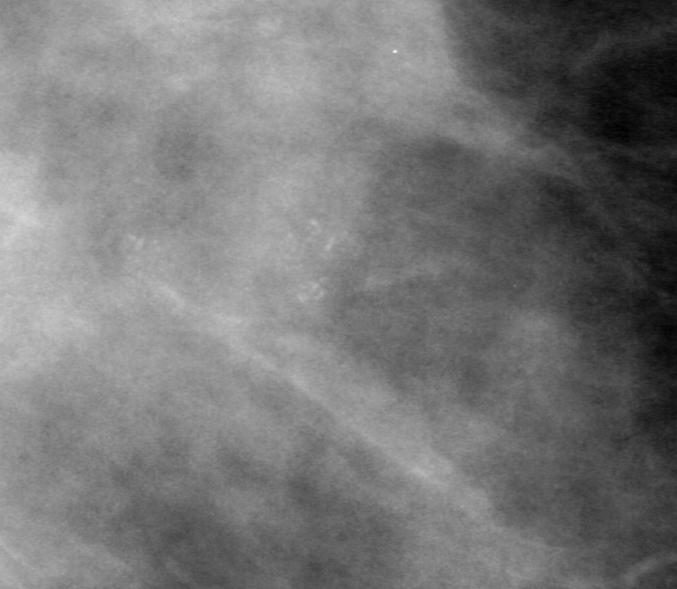
Region of interest cut from a scanned film mammogram (one marked finding), right breast, CC view, BI-RADS breast density category 3 (scale 1–4).
Finding: calcifications, morphology amorphous, distribution clustered; BI-RADS assessment category 3; subtlety rating 3 on a 1 (subtle) to 5 (obvious) scale; pathology result (as recorded, not read from the image): malignant.